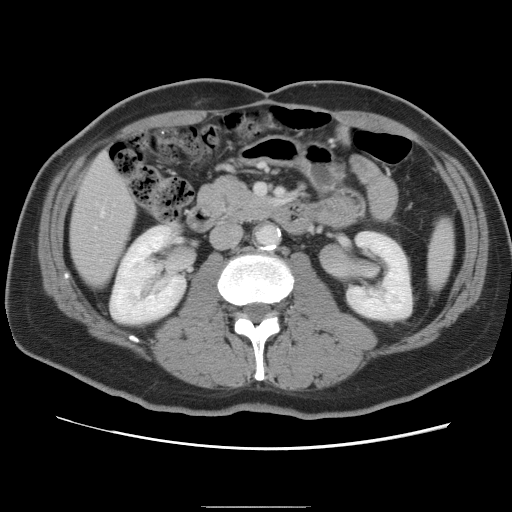
Contrast-enhanced abdominal CT, one axial slice. 120 kVp. Intravenous contrast given. Soft-tissue window (W 400 / L 40 HU). 5 mm slice thickness. 512 × 512 image matrix, field of view 363 × 363 mm. Male patient, age 63 years. Case-level facts recorded for this patient, not image findings: diagnosis: colorectal cancer liver metastases, imaged before liver resection; multiple liver metastases: no; largest metastasis: 9 cm; disease in both lobes: no.
Structures marked on this image (outlined manually by an expert reader):
- hepatic veins: bounding box <101,210,104,215> (left, top, right, bottom; pixels)
- liver: <72,155,136,285>
- planned liver remnant (the part of the liver to remain after resection): <72,155,136,285>